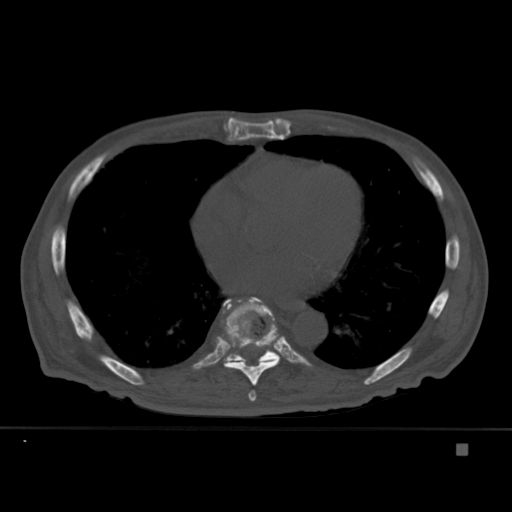
CT including the spine, one axial slice. Bone window (W 1800 / L 400 HU). 1.5 mm slice thickness. 512 × 512 image matrix, field of view 378 × 378 mm. Male patient, age 75 years. Case-level facts recorded for this patient, not image findings: primary cancer: prostate.
Outlined on this slice (semi-automatically segmented with operator editing):
- T7 vertebra: bounding box [x1, y1, x2, y2] px = [248, 390, 257, 402]
- T8 vertebra: [221, 297, 280, 386]
- T9 vertebra: [224, 321, 279, 367]